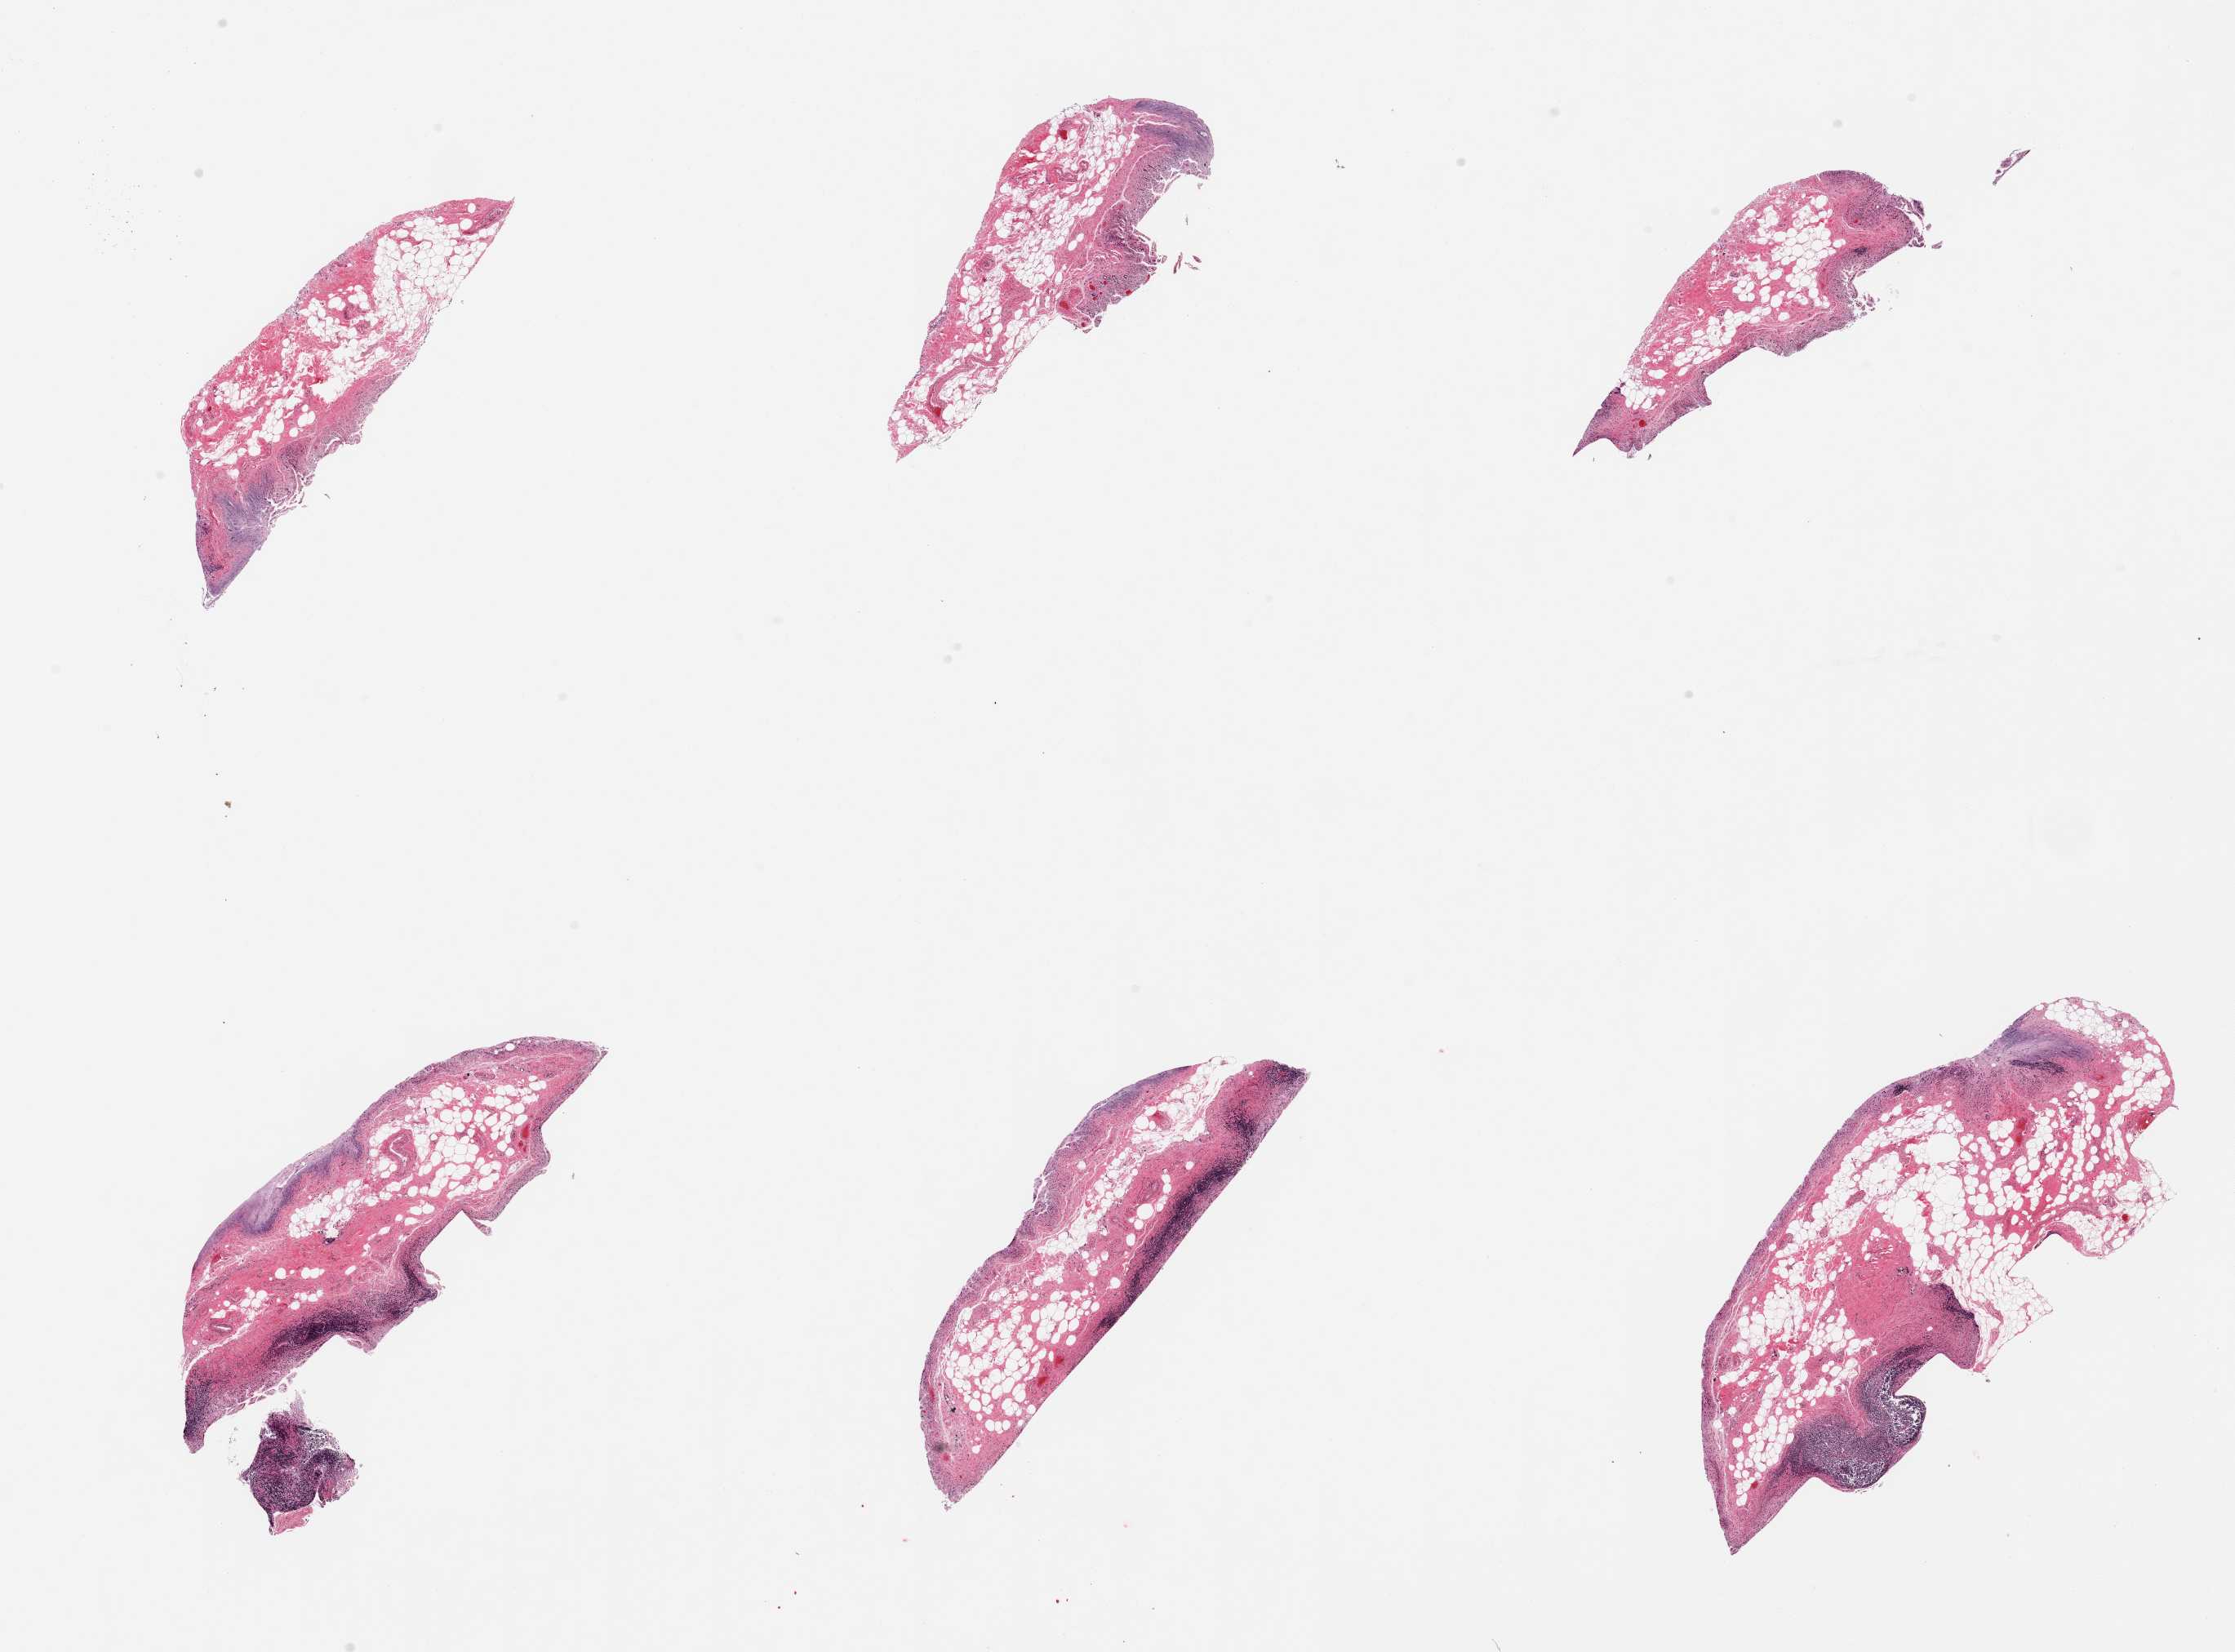
Digitized haematoxylin and eosin-stained section, whole scanned area (about 21.7 x 16.0 mm) shown as a low-resolution overview. Donor: male.
- specimen: PAXgene-fixed, paraffin-embedded tissue; target tissue: ileum; tissue donor sample